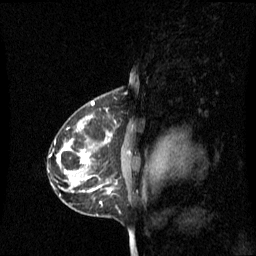
Breast MRI (dynamic contrast-enhanced), one sagittal slice. Slice 42 of 60 in the series (ordered by position). Dynamic contrast-enhanced series, image 2 of 3 at this slice position (ordered by acquisition). 1.5 T. TE 4.2 ms, TR 8.4 ms. 256 × 256 image matrix. Patient: female, 42 years. Case-level facts recorded for this patient, not image findings: setting: breast cancer imaged before/during neoadjuvant chemotherapy; receptor status: HR-positive, HER2-negative.
Outlined on this slice (semi-automatic segmentation, software-assisted and operator-edited):
- analysis volume of interest (the breast-tissue region the enhancement analysis was run in; not a lesion): bounding box (x1, y1, x2, y2) in pixels: (68, 110, 137, 193)
- tumour enhancement mask (voxels above the 70 % enhancement threshold inside the analysis volume of interest): (80, 152, 111, 191)